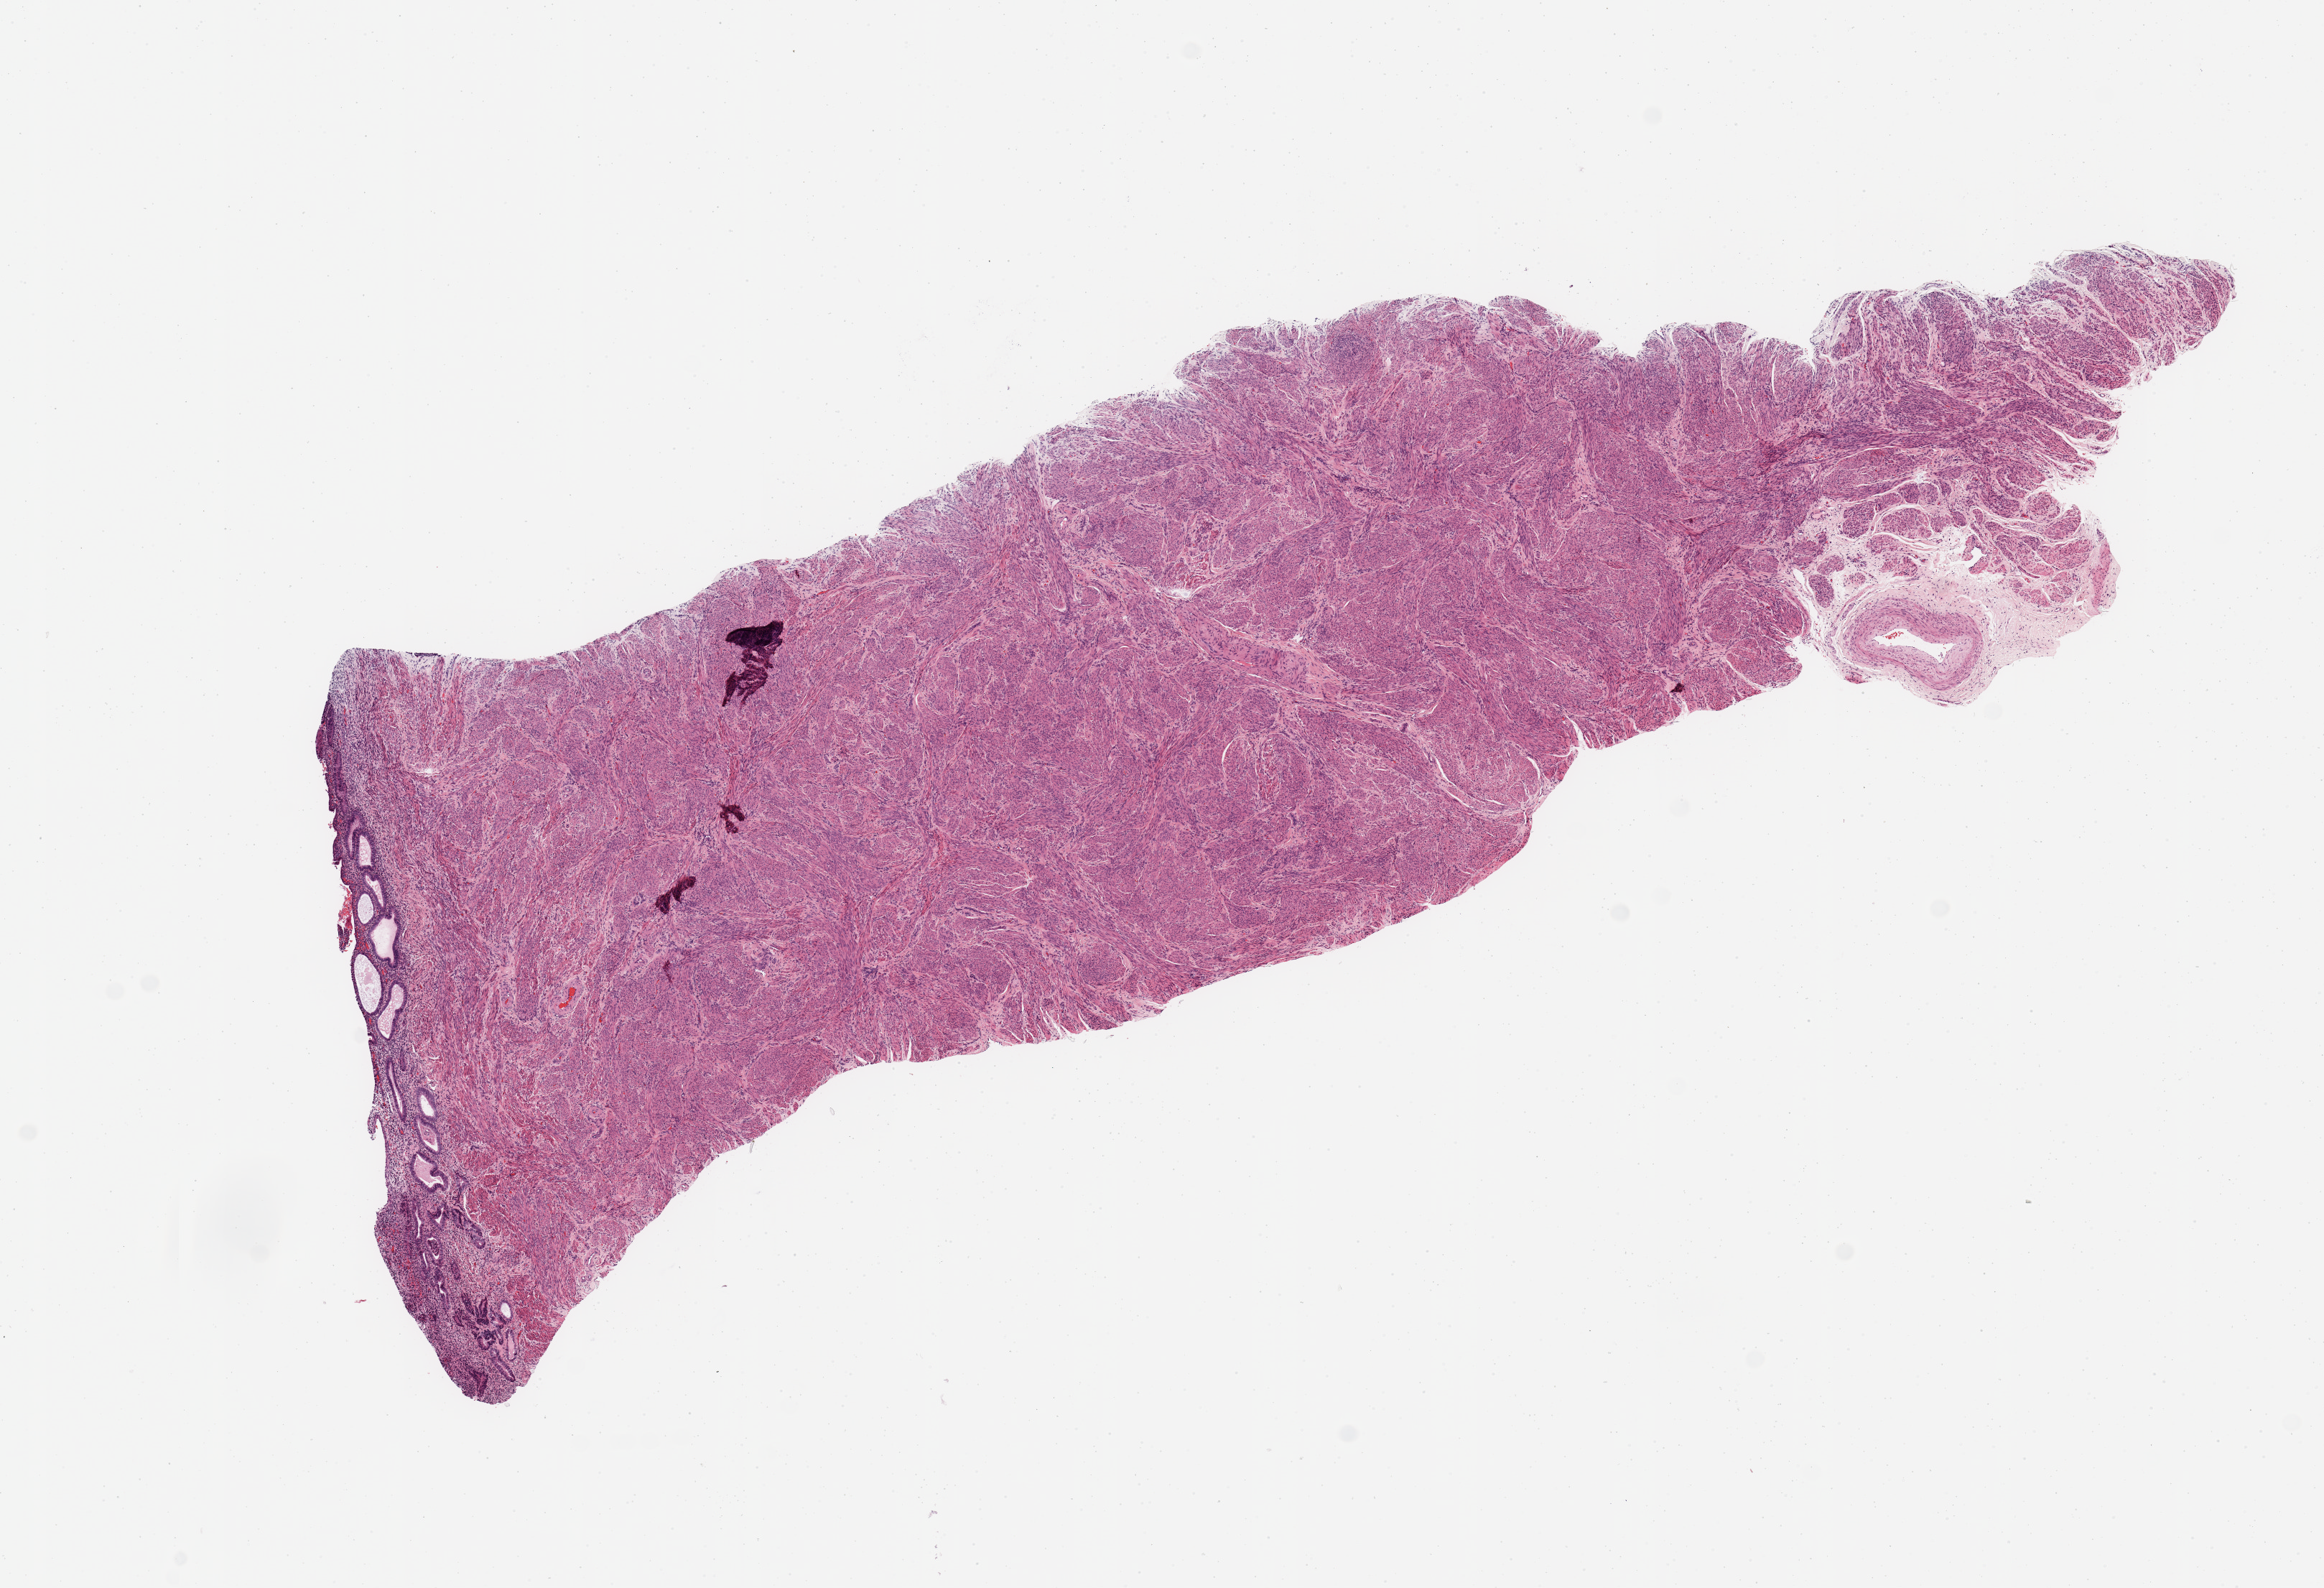
Digitized H&E tissue section (whole slide) — shown as a low-resolution overview of the whole scanned area (about 12.8 x 8.7 mm, from a 20x scan). Normal (non-tumour) tissue sample, sampled site: uterus. 64-year-old female patient.
• this section: normal (non-tumour) tissue from the same patient
• patient diagnosis: Endometrioid adenocarcinoma, NOS